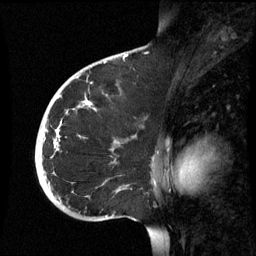
Breast MRI (dynamic contrast-enhanced), one sagittal slice. Slice 38 of 60 in the series (ordered by position). Dynamic contrast-enhanced series, image 2 of 3 at this slice position (ordered by acquisition). 1.5 T. TE 4.2 ms, TR 8.9 ms. 2.6 mm slice thickness. 256 × 256 image matrix, field of view 220 × 220 mm. Patient: female, 35 years. Case-level facts recorded for this patient, not image findings: setting: breast cancer imaged before/during neoadjuvant chemotherapy; receptor status: HR-positive, HER2-negative.
Outlined on this slice (semi-automatic segmentation, software-assisted and operator-edited):
- analysis volume of interest (the breast-tissue region the enhancement analysis was run in; not a lesion): box from (x=35, y=74) to (x=160, y=221) px
- tumour enhancement mask (voxels above the 70 % enhancement threshold inside the analysis volume of interest): (x=54, y=100)–(x=91, y=147)